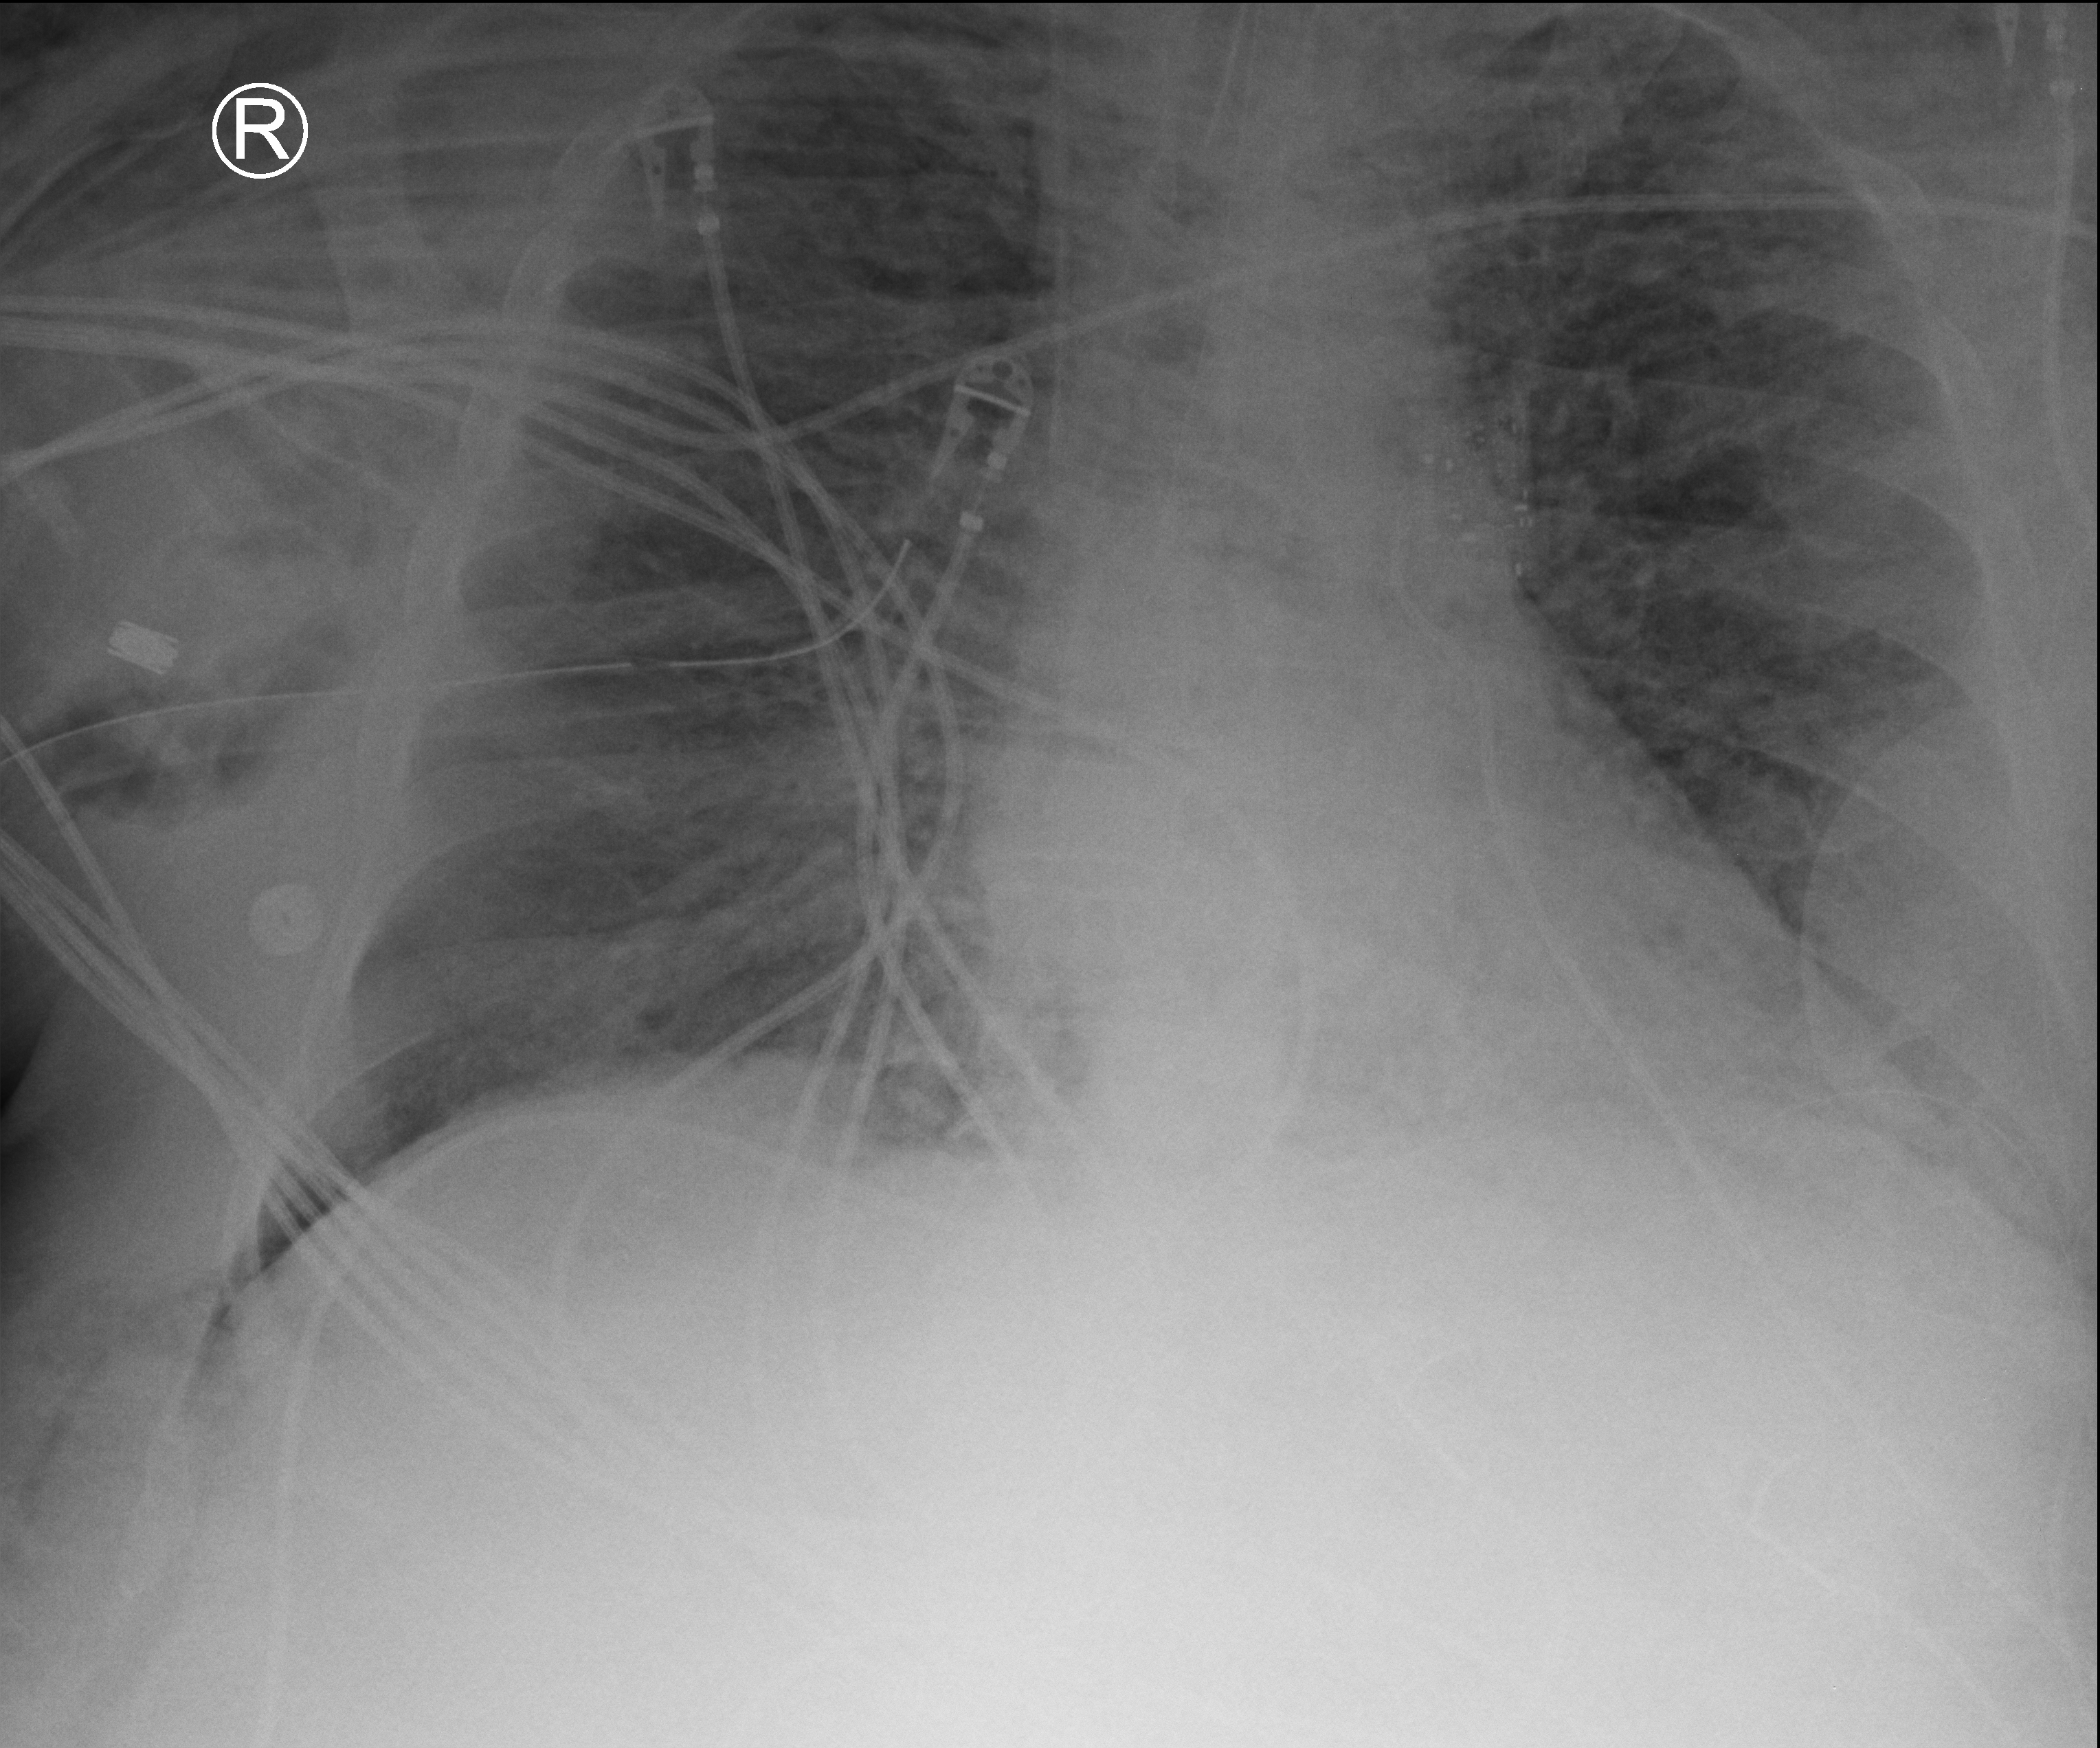
Chest X-ray (portable). Adult patient hospitalised with COVID-19, age 18–59 years.
Hospital-stay facts (about this admission, not read from this image; timing relative to this image not recorded): COPD (admission record): no.